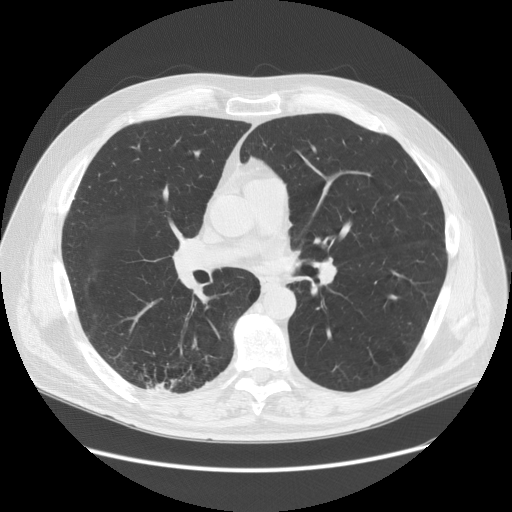
Low-dose screening chest CT, one axial slice; position 78 of 149 along the scan axis; reconstruction kernel STANDARD; 120 kVp; lung window (W 1500 / L -600 HU); 2.5 mm slice thickness; 512 × 512 image matrix, field of view 400 × 400 mm.
Outlined on this slice (manually delineated by an expert):
- lesion 1 (tumor, lower lobe of right lung): bounding box (x1, y1, x2, y2) in pixels: (147, 379, 176, 392)